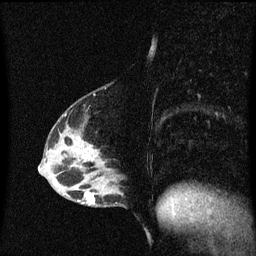
Breast MRI (dynamic contrast-enhanced), one sagittal slice. Position 23 of 60 along the scan axis. Dynamic contrast-enhanced series, image 2 of 3 at this slice position (ordered by acquisition). 1.5 T. TE 4.2 ms, TR 8.4 ms. 256 × 256 image matrix, field of view 200 × 200 mm. Patient: female, 40 years.
Annotated regions visible in this slice (semi-automatic segmentation, software-assisted and operator-edited):
- analysis volume of interest (the breast-tissue region the enhancement analysis was run in; not a lesion): bounding box [x1, y1, x2, y2] px = [82, 172, 126, 207]
- tumour enhancement mask (voxels above the 70 % enhancement threshold inside the analysis volume of interest): [85, 192, 96, 205]